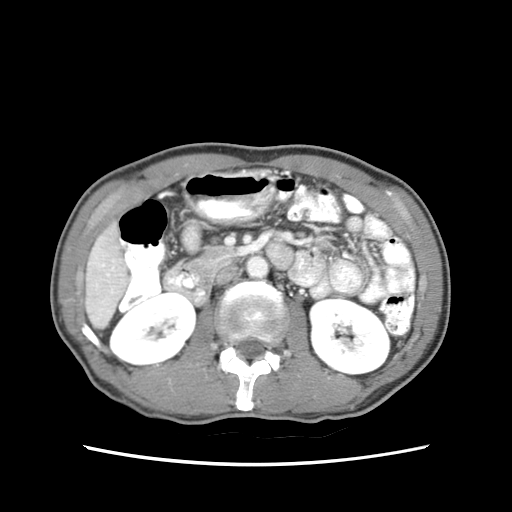
Contrast-enhanced abdominal CT (liver protocol), one axial slice. Reconstruction kernel STANDARD. 120 kVp. Soft-tissue window (W 400 / L 40 HU). 2.5 mm slice thickness. 512 × 512 image matrix, field of view 320 × 320 mm. From the clinical record (not read from this slice): diagnosis: hepatocellular carcinoma (patient treated with transarterial chemoembolisation; whether this scan precedes or follows treatment is not stated here); TNM stage (as recorded): Stage-IIIB; Child-Pugh class: A.
Structures marked on this image (semi-automatically segmented with operator editing):
- liver parenchyma outside the tumour (the mass and vessels are separate outlines, so this box may not span the whole liver): bounding box <86,224,128,326> (left, top, right, bottom; pixels)
- liver vessels: <96,239,115,313>